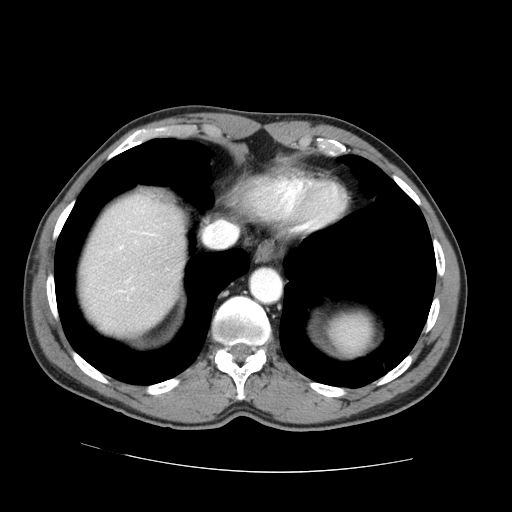
Contrast-enhanced abdominal CT (liver protocol), one axial slice; position 63 of 73 along the scan axis; 100 kVp; one of 2 acquisitions stored at this slice position; soft-tissue window (W 400 / L 40 HU); 512 × 512 image matrix, field of view 380 × 380 mm. Case-level facts recorded for this patient, not image findings: diagnosis: hepatocellular carcinoma (patient treated with transarterial chemoembolisation; whether this scan precedes or follows treatment is not stated here); TNM stage (as recorded): Stage-IVA; Child-Pugh class: A.
Structures marked on this image (semi-automatic segmentation, software-assisted and operator-edited):
- abdominal aorta: bounding box [x1, y1, x2, y2] px = [252, 269, 280, 302]
- liver parenchyma outside the tumour (the mass and vessels are separate outlines, so this box may not span the whole liver): [80, 196, 184, 334]
- liver vessels: [120, 246, 123, 248]